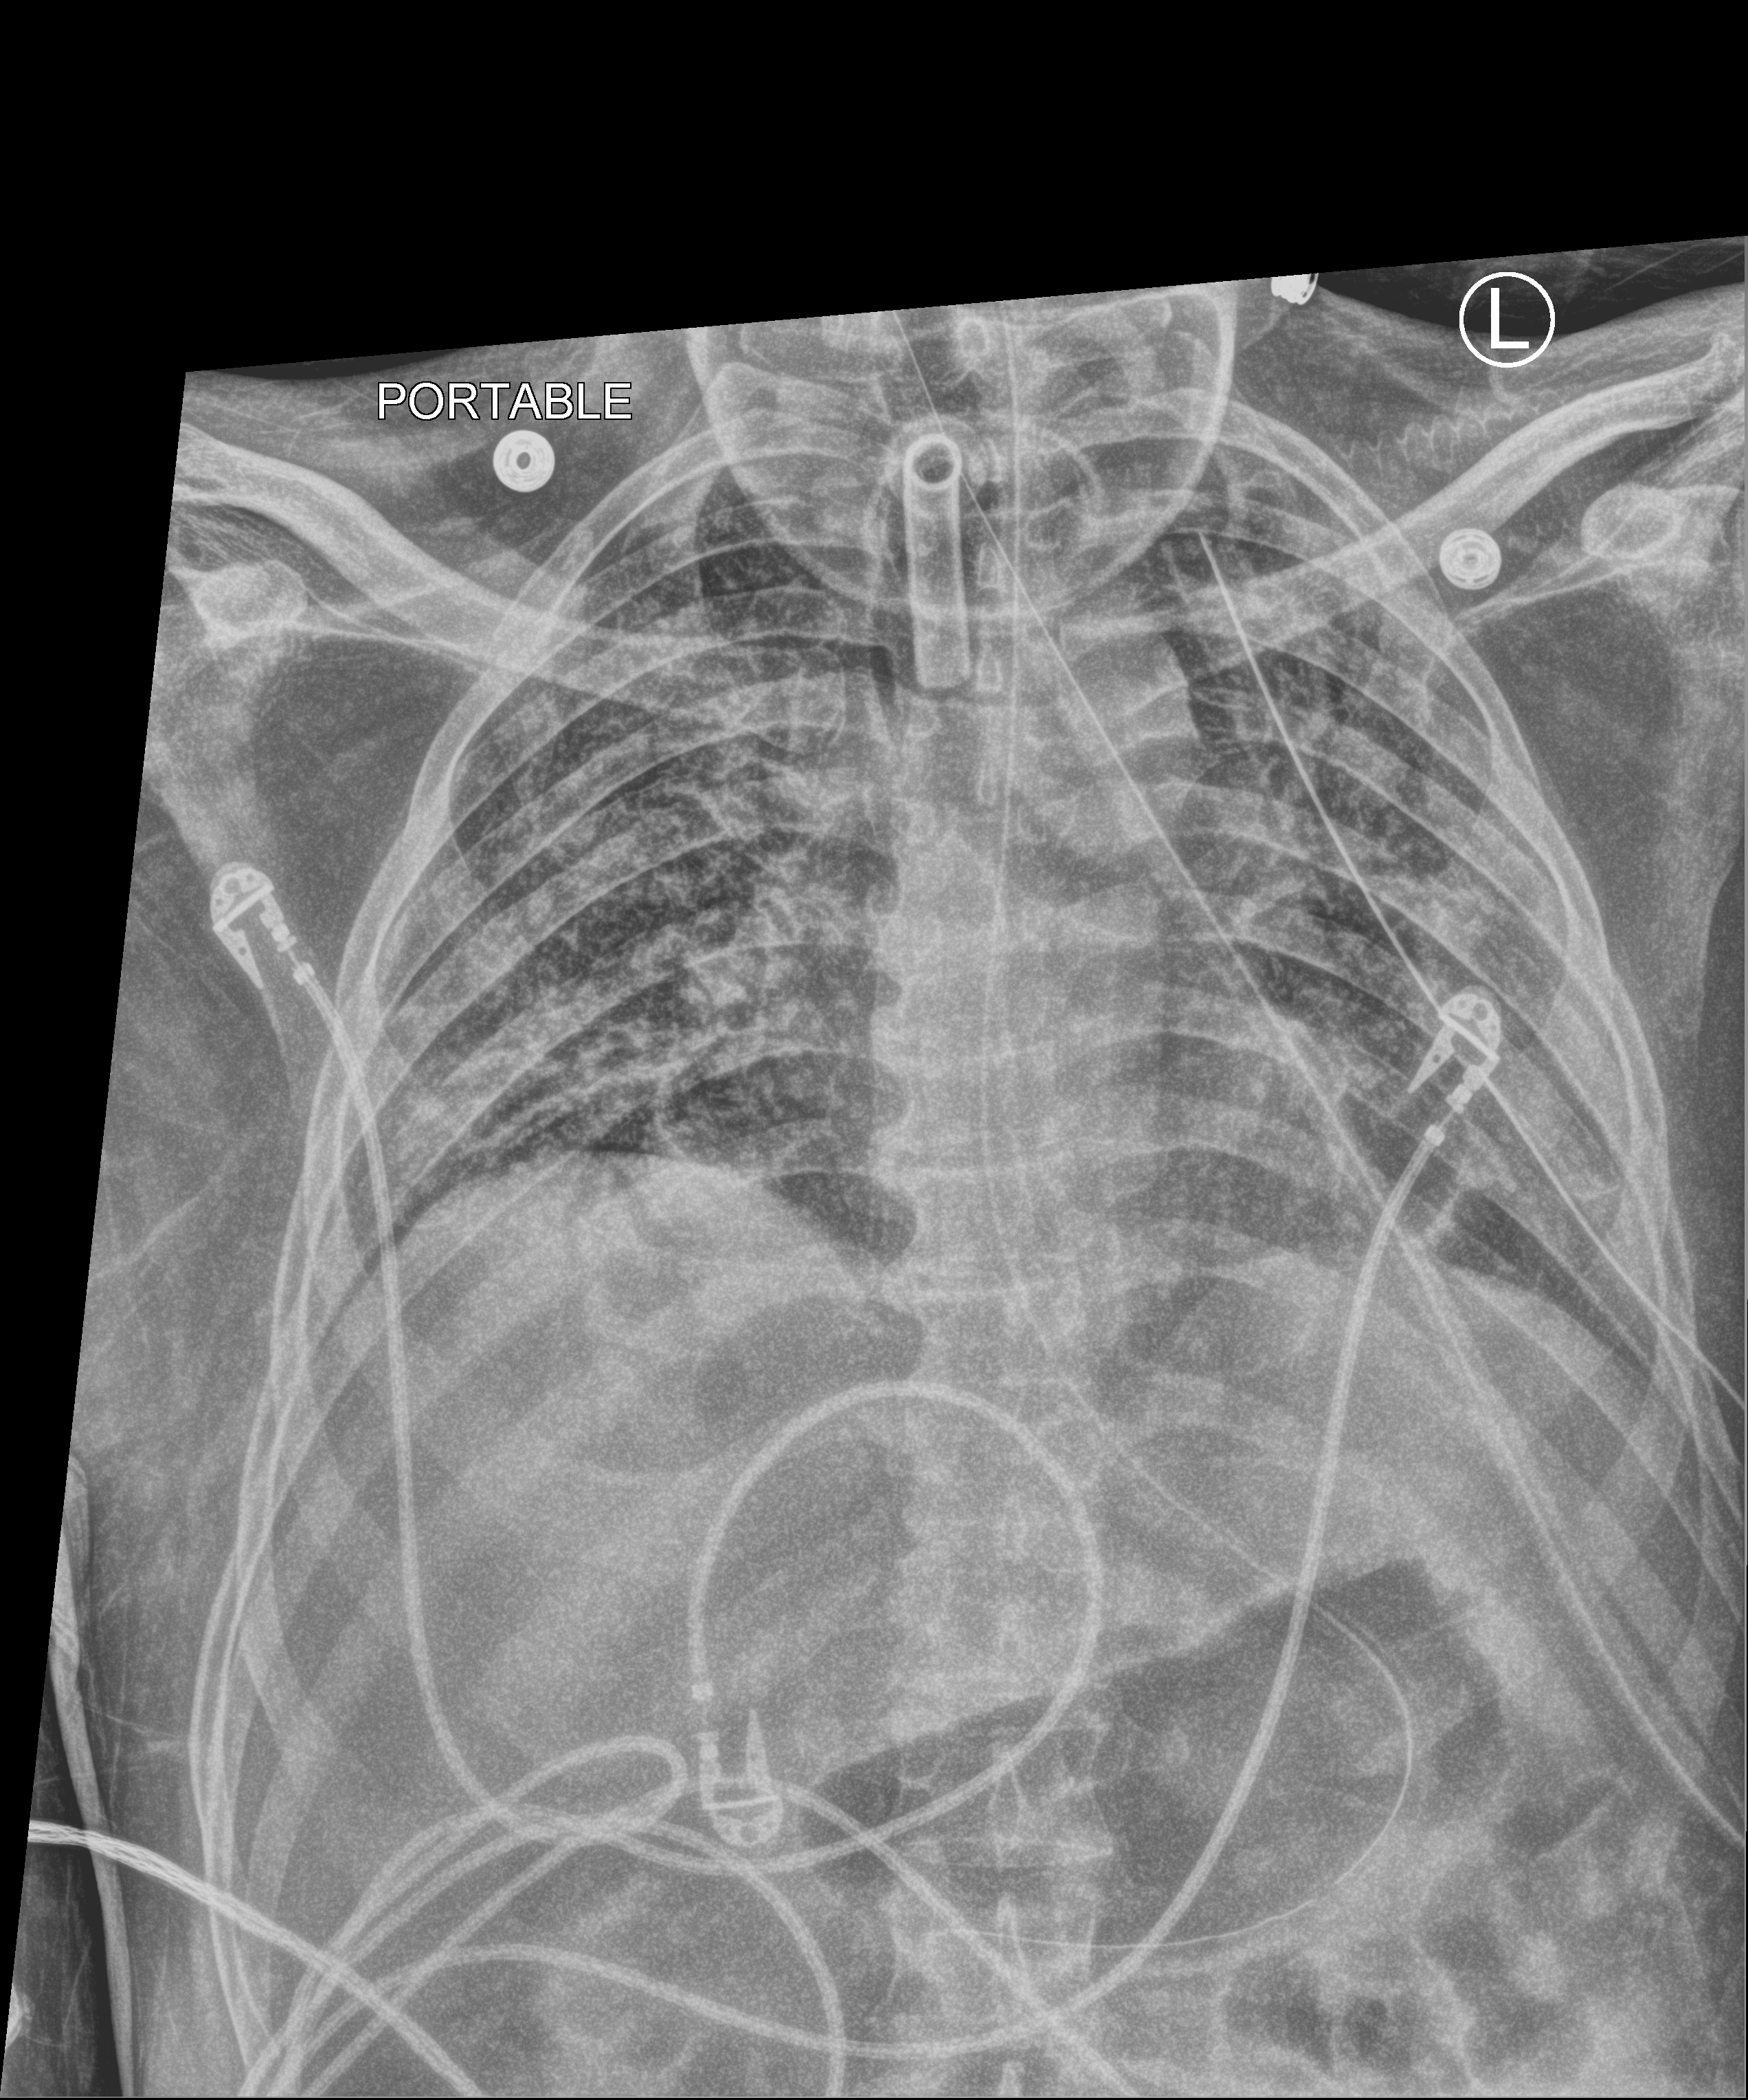
Bedside chest radiograph (computed radiography), anteroposterior (AP) projection. Patient hospitalised with COVID-19; male, aged 18–59 years.
Hospital-stay facts (about this admission, not read from this image; timing relative to this image not recorded):
- diabetes (admission record): no
- length of hospital stay: 83 days